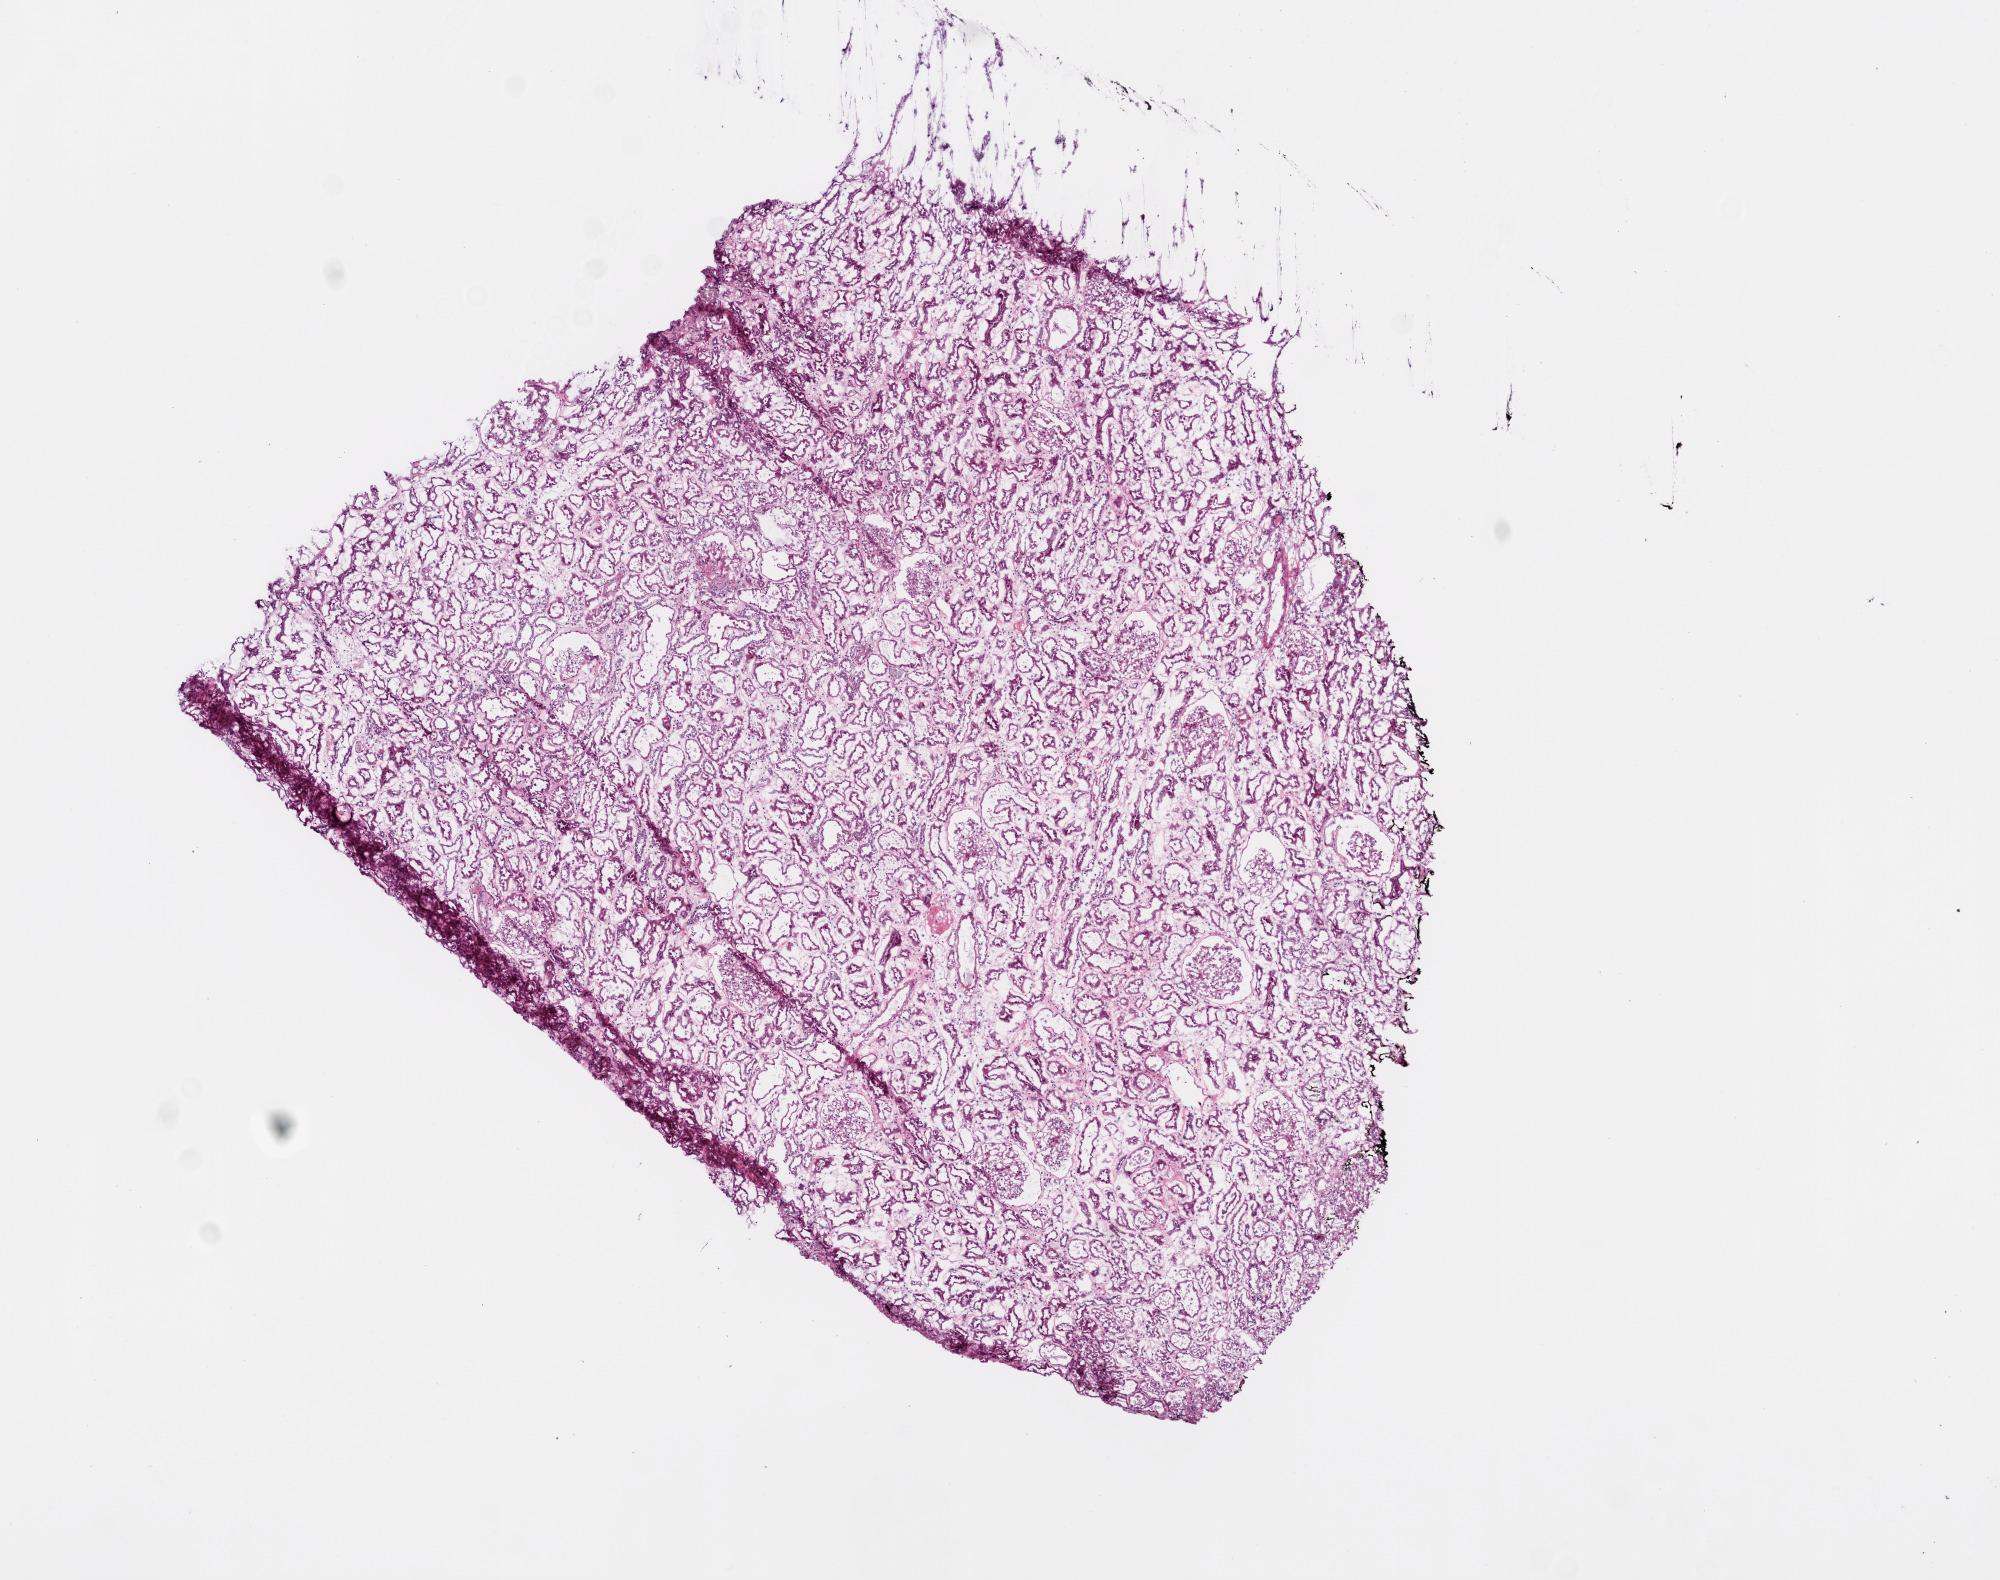
Hematoxylin and eosin (H&E) stained whole-slide image, a low-resolution overview of the entire scanned area, about 8.0 x 6.3 mm (acquisition: 20x scan); frozen section from the top of the tissue portion; solid tissue normal (non-tumour tissue) sample from the kidney. Patient: female, age at initial diagnosis 46 years.
This section: solid tissue normal (non-tumour) sample from the same patient. Patient diagnosis: Clear cell adenocarcinoma, NOS.